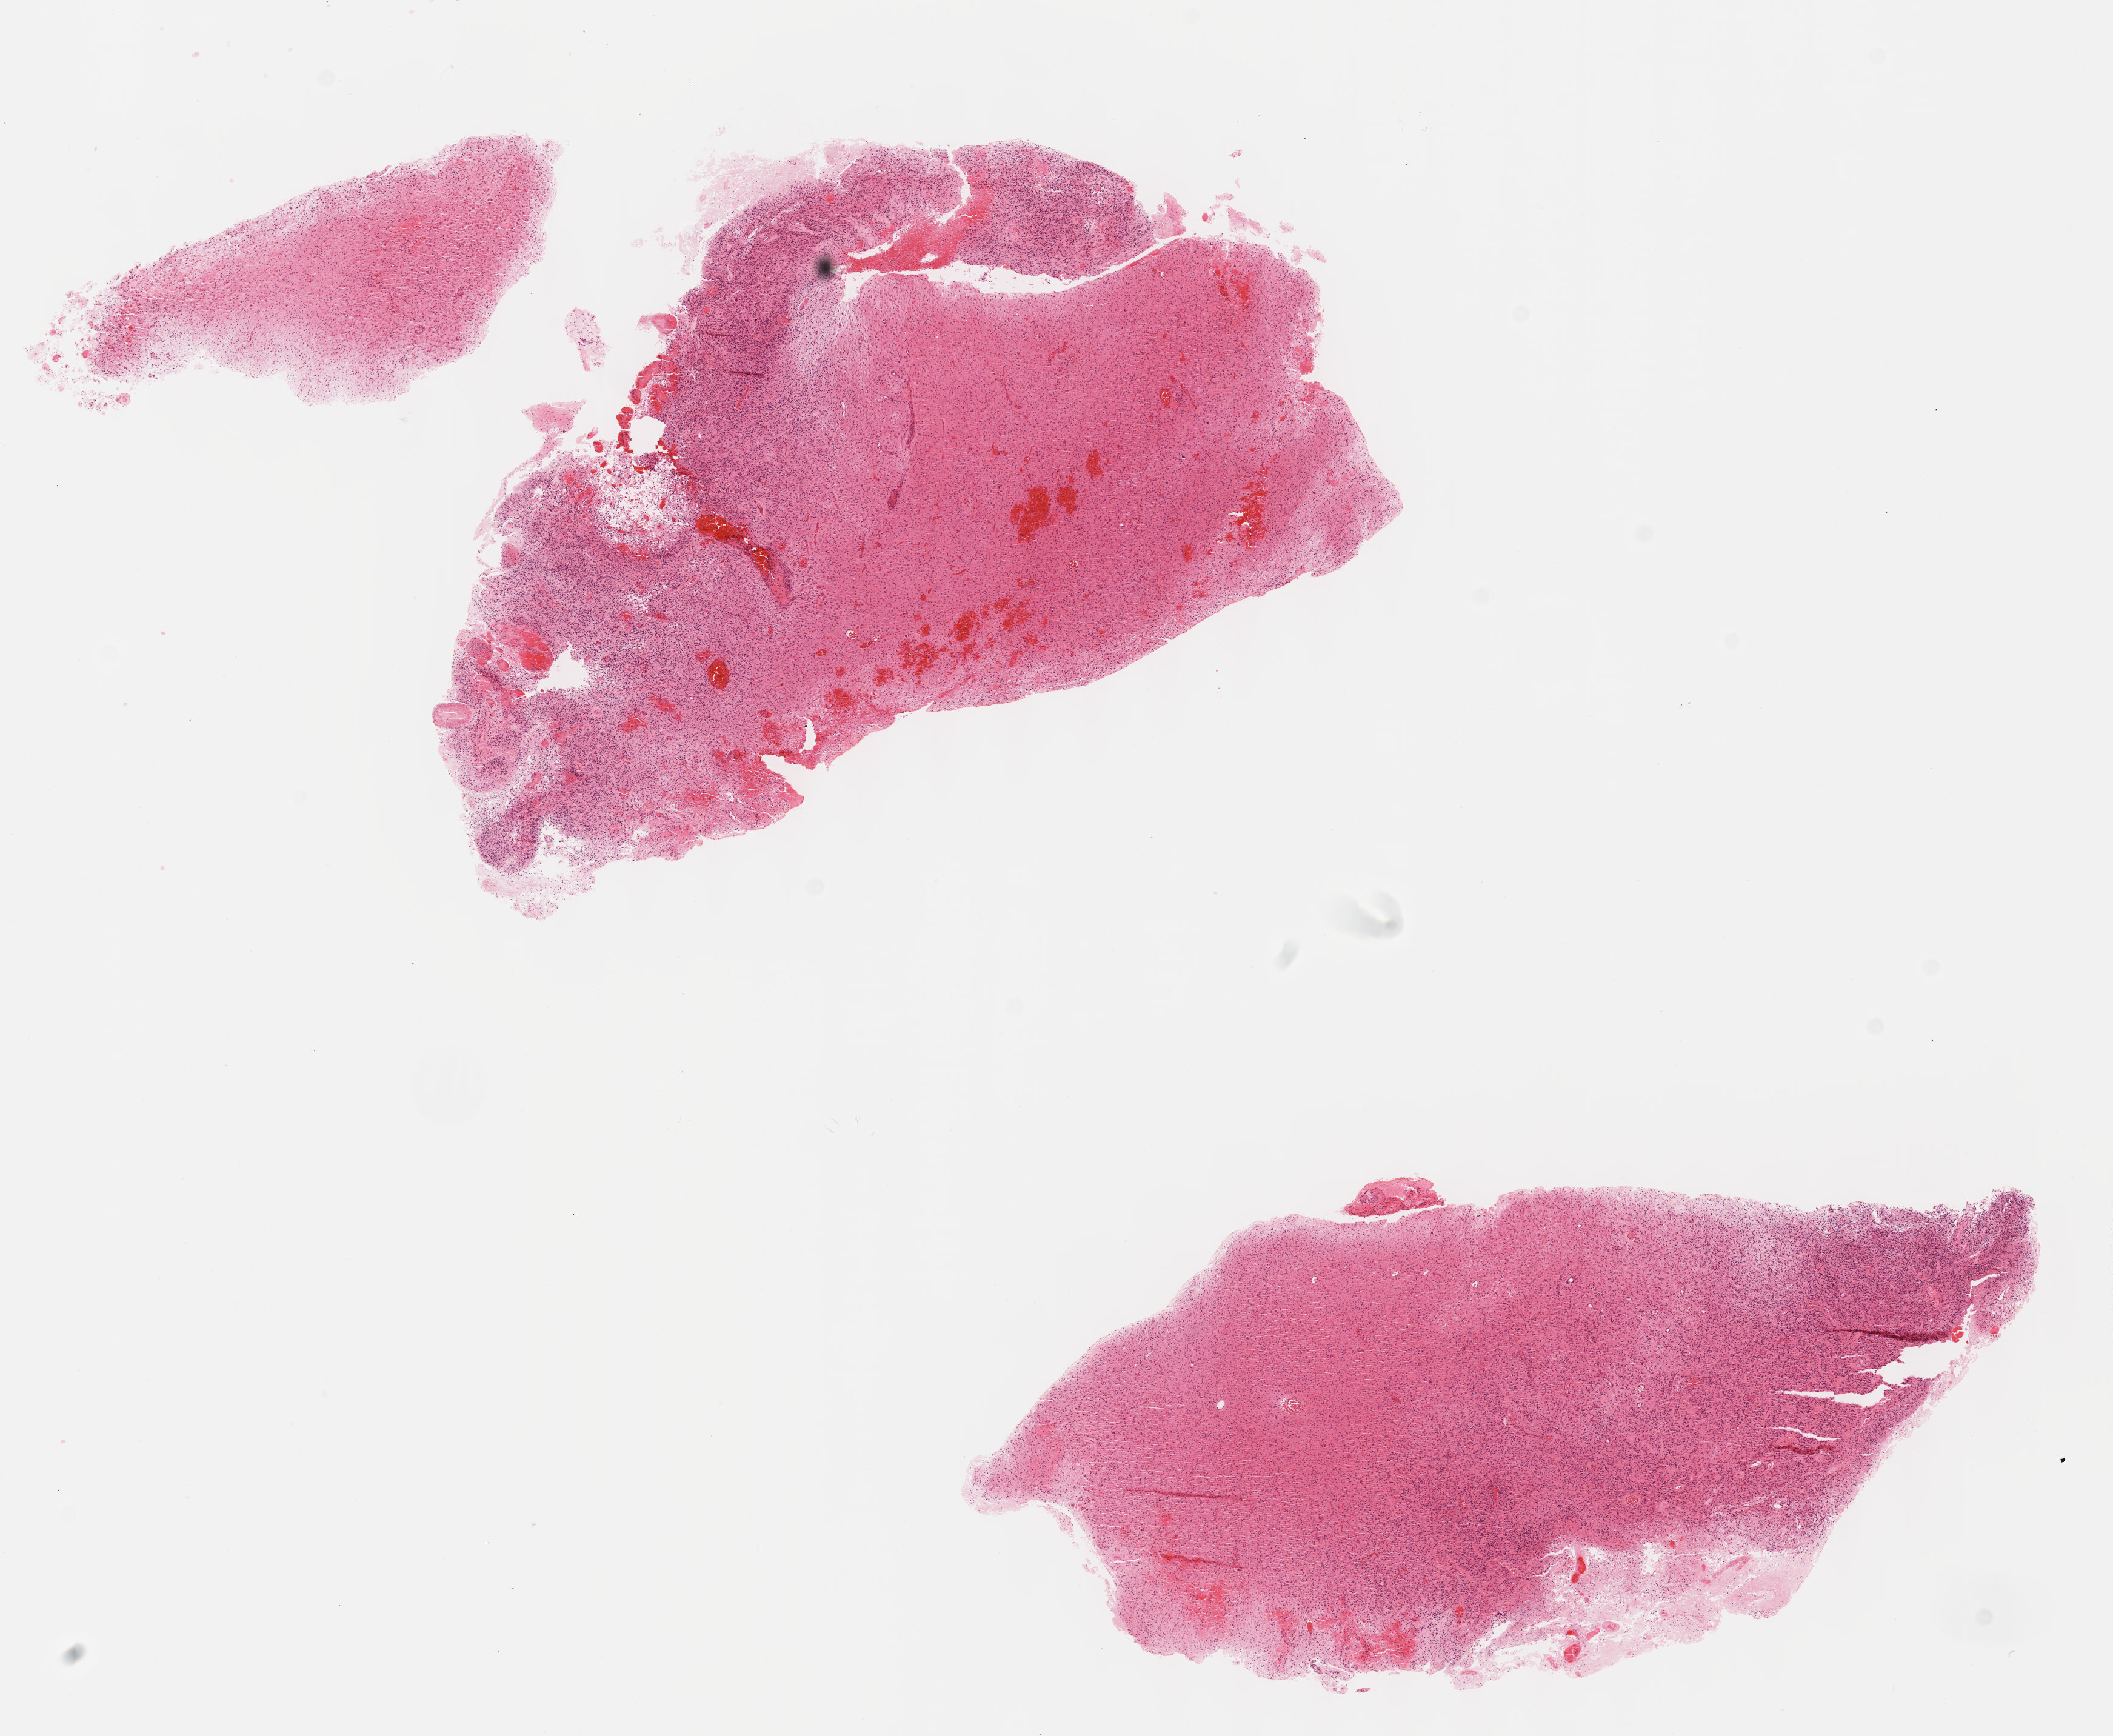
Digitized Hematoxylin and eosin (H&E) stained tissue section (whole slide), shown as a low-resolution overview of the whole scanned area (about 14.1 x 11.6 mm, acquisition: 40x scan); formalin-fixed paraffin-embedded (FFPE) diagnostic section; sample: primary tumour, brain. Male, age 64 years at initial diagnosis.
• histologic diagnosis: Glioblastoma